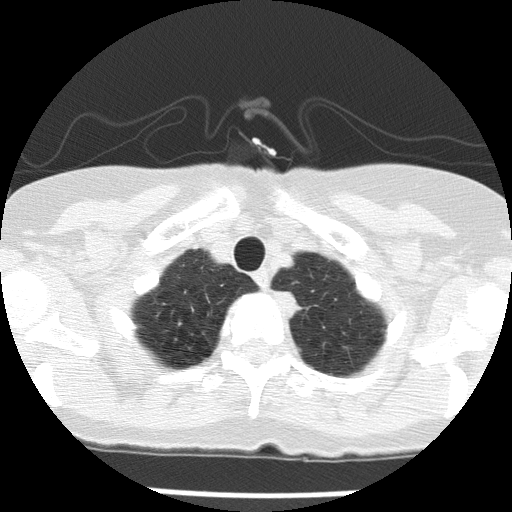
Chest CT (low-dose screening protocol), one axial image; baseline annual screen; lung window (W 1500 / L -600 HU); 2 mm slice thickness; lung (sharp) reconstruction kernel (FC51); slice 15 of 143 in the series; 512 × 512 image matrix. Female, age 74 years at enrolment. Former smoker at enrolment.
Lesion marked by an expert reader, bounding box <268,287,306,319> (left, top, right, bottom; pixels). The screening reader recorded 2 non-calcified nodules or masses ≥4 mm on this exam; which of them this box marks is not recorded.